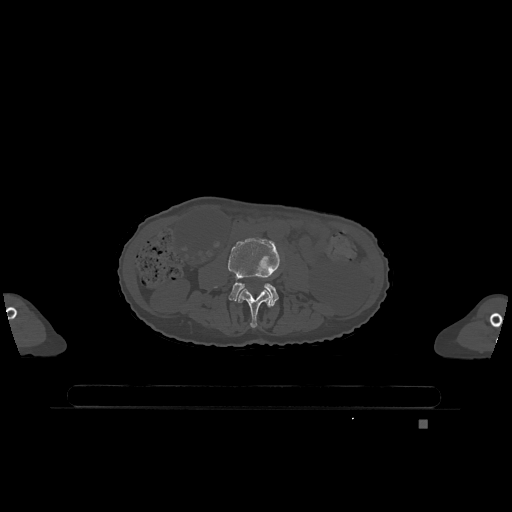
CT including the spine, one axial slice; position 328 of 1317 along the scan axis; bone window (W 1800 / L 400 HU); 0.5 mm slice thickness; 512 × 512 image matrix. Patient: female, 74 years. Case-level facts recorded for this patient, not image findings: primary cancer: lung; vertebrae with lytic lesions (as recorded): T1, T4, T5, T6, L4, L5.
Annotated regions visible in this slice (semi-automatically segmented with operator editing):
- L3 vertebra: bounding box [x1, y1, x2, y2] px = [238, 288, 271, 328]
- L4 vertebra: [228, 237, 279, 306]